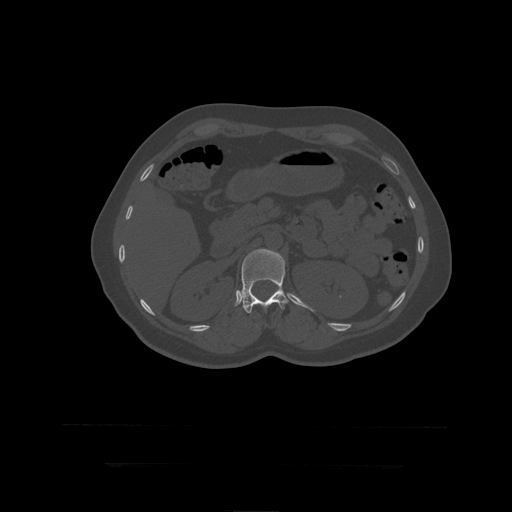
CT including the spine, one axial slice; slice 174 of 399 in the series (ordered by position); reconstruction kernel STANDARD; bone window (W 1800 / L 400 HU); 512 × 512 image matrix, field of view 450 × 450 mm. Patient age 41 years. Case-level facts recorded for this patient, not image findings: primary cancer: breast.
Annotated regions visible in this slice (semi-automatic segmentation, software-assisted and operator-edited):
- L1 vertebra: bounding box (x1, y1, x2, y2) in pixels: (242, 249, 289, 314)